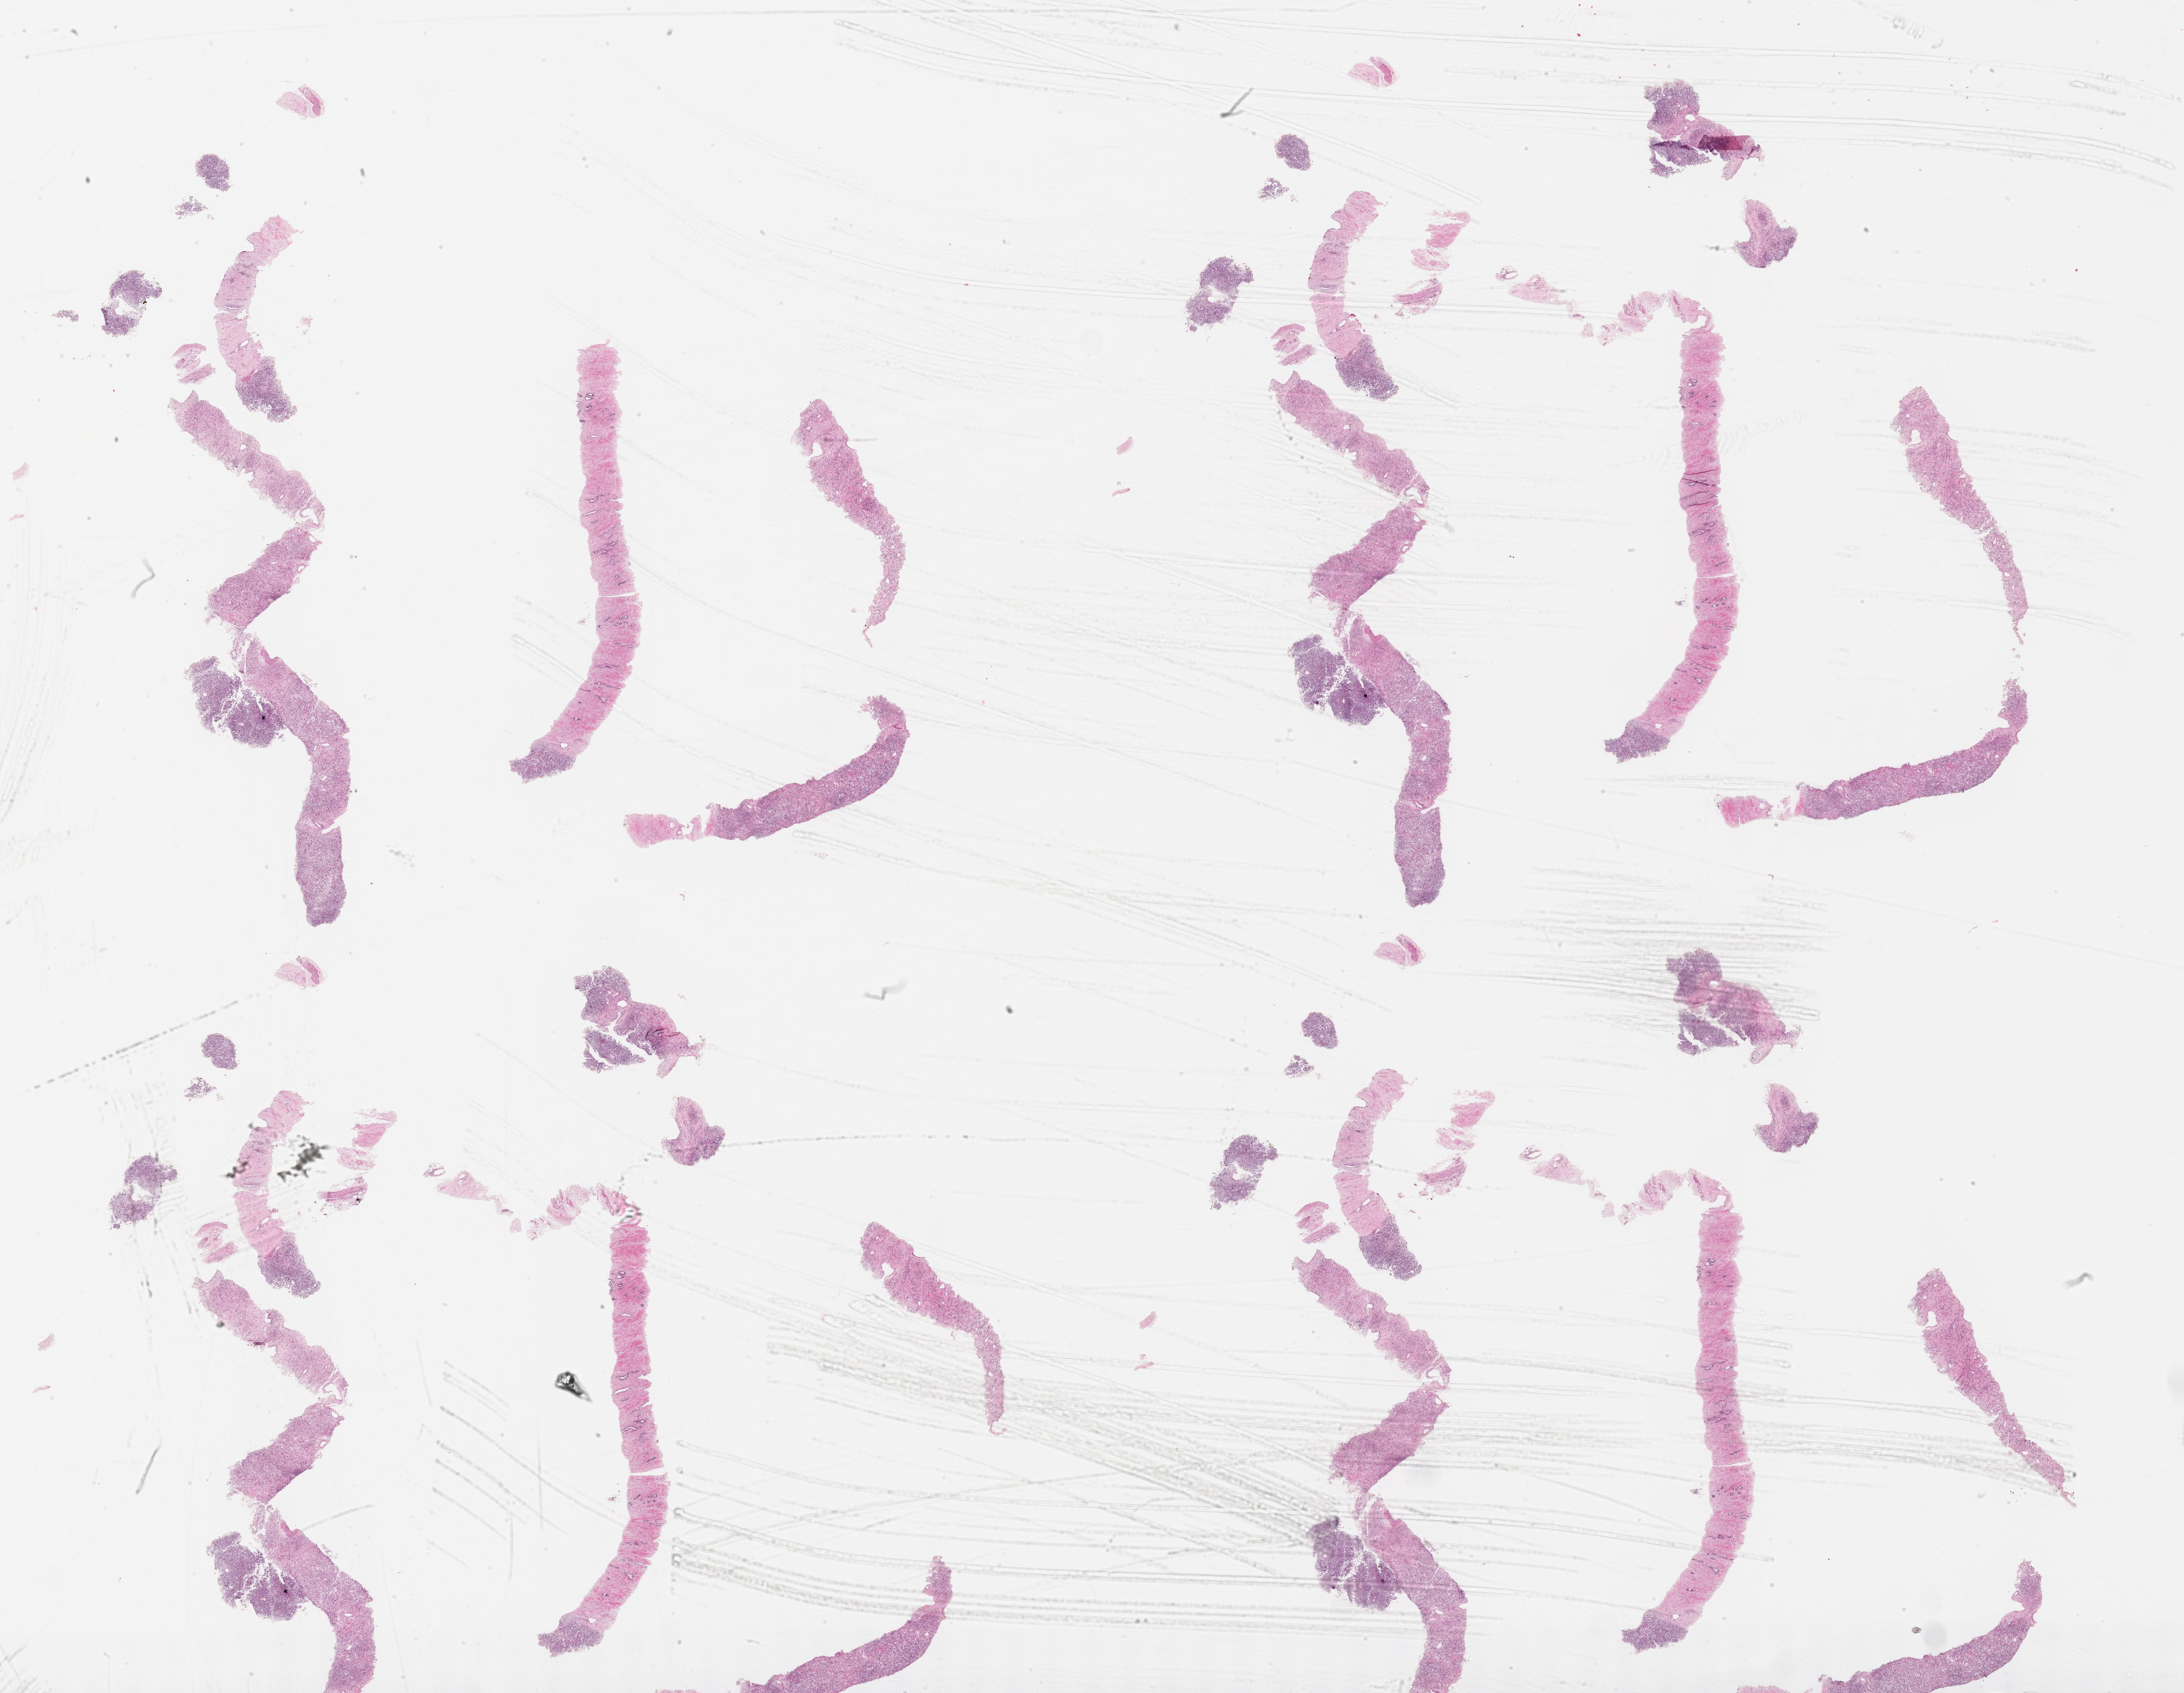
H&E whole-slide image of tumor tissue, a low-resolution overview of the entire scanned area, about 28.7 x 22.2 mm; FFPE section; sample anatomic site: prostate. Male patient, age at diagnosis 19.6 years.
Metastatic status at presentation (as recorded): non-metastatic (unconfirmed). Diagnosis: rhabdomyosarcoma; histological classification: embryonal rhabdomyosarcoma.